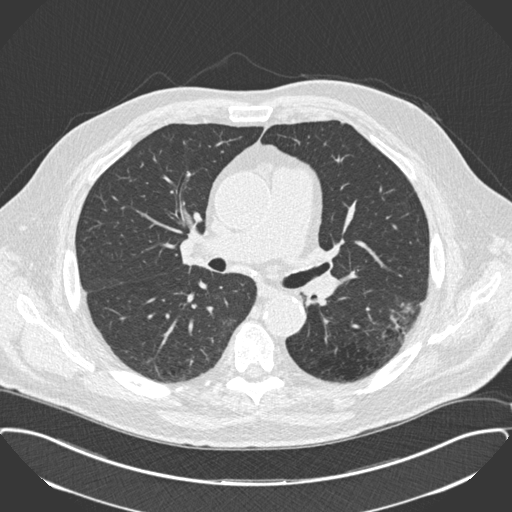
Low-dose screening chest CT, one axial slice; slice 101 of 175 in the series (ordered by position); reconstruction kernel B30f; lung window (W 1500 / L -600 HU); 2 mm slice thickness; 512 × 512 image matrix.
Outlined on this slice (manually delineated by an expert):
- lesion 1 (tumor, lower lobe of left lung): bounding box [x1, y1, x2, y2] px = [390, 301, 416, 336]